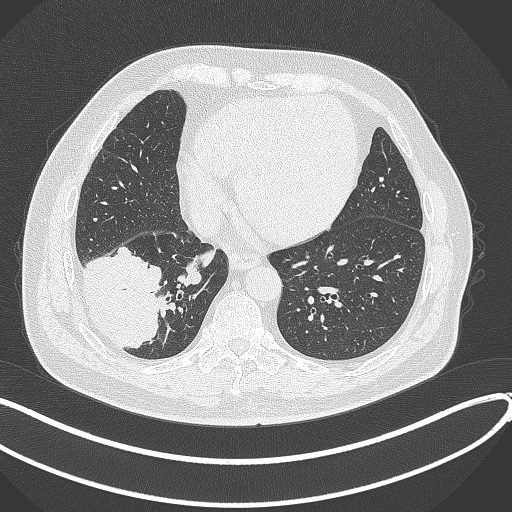
Chest CT, one axial slice; position 113 of 360 along the scan axis; reconstruction kernel B70f; 120 kVp; lung window (W 1500 / L -600 HU); 1 mm slice thickness; 512 × 512 image matrix, field of view 400 × 400 mm. Patient: male, 59 years.
Outlined on this slice (rectangle marked by the reading radiologist):
- lung tumour (recorded histology: adenocarcinoma): bounding box <82,243,176,352> (left, top, right, bottom; pixels)